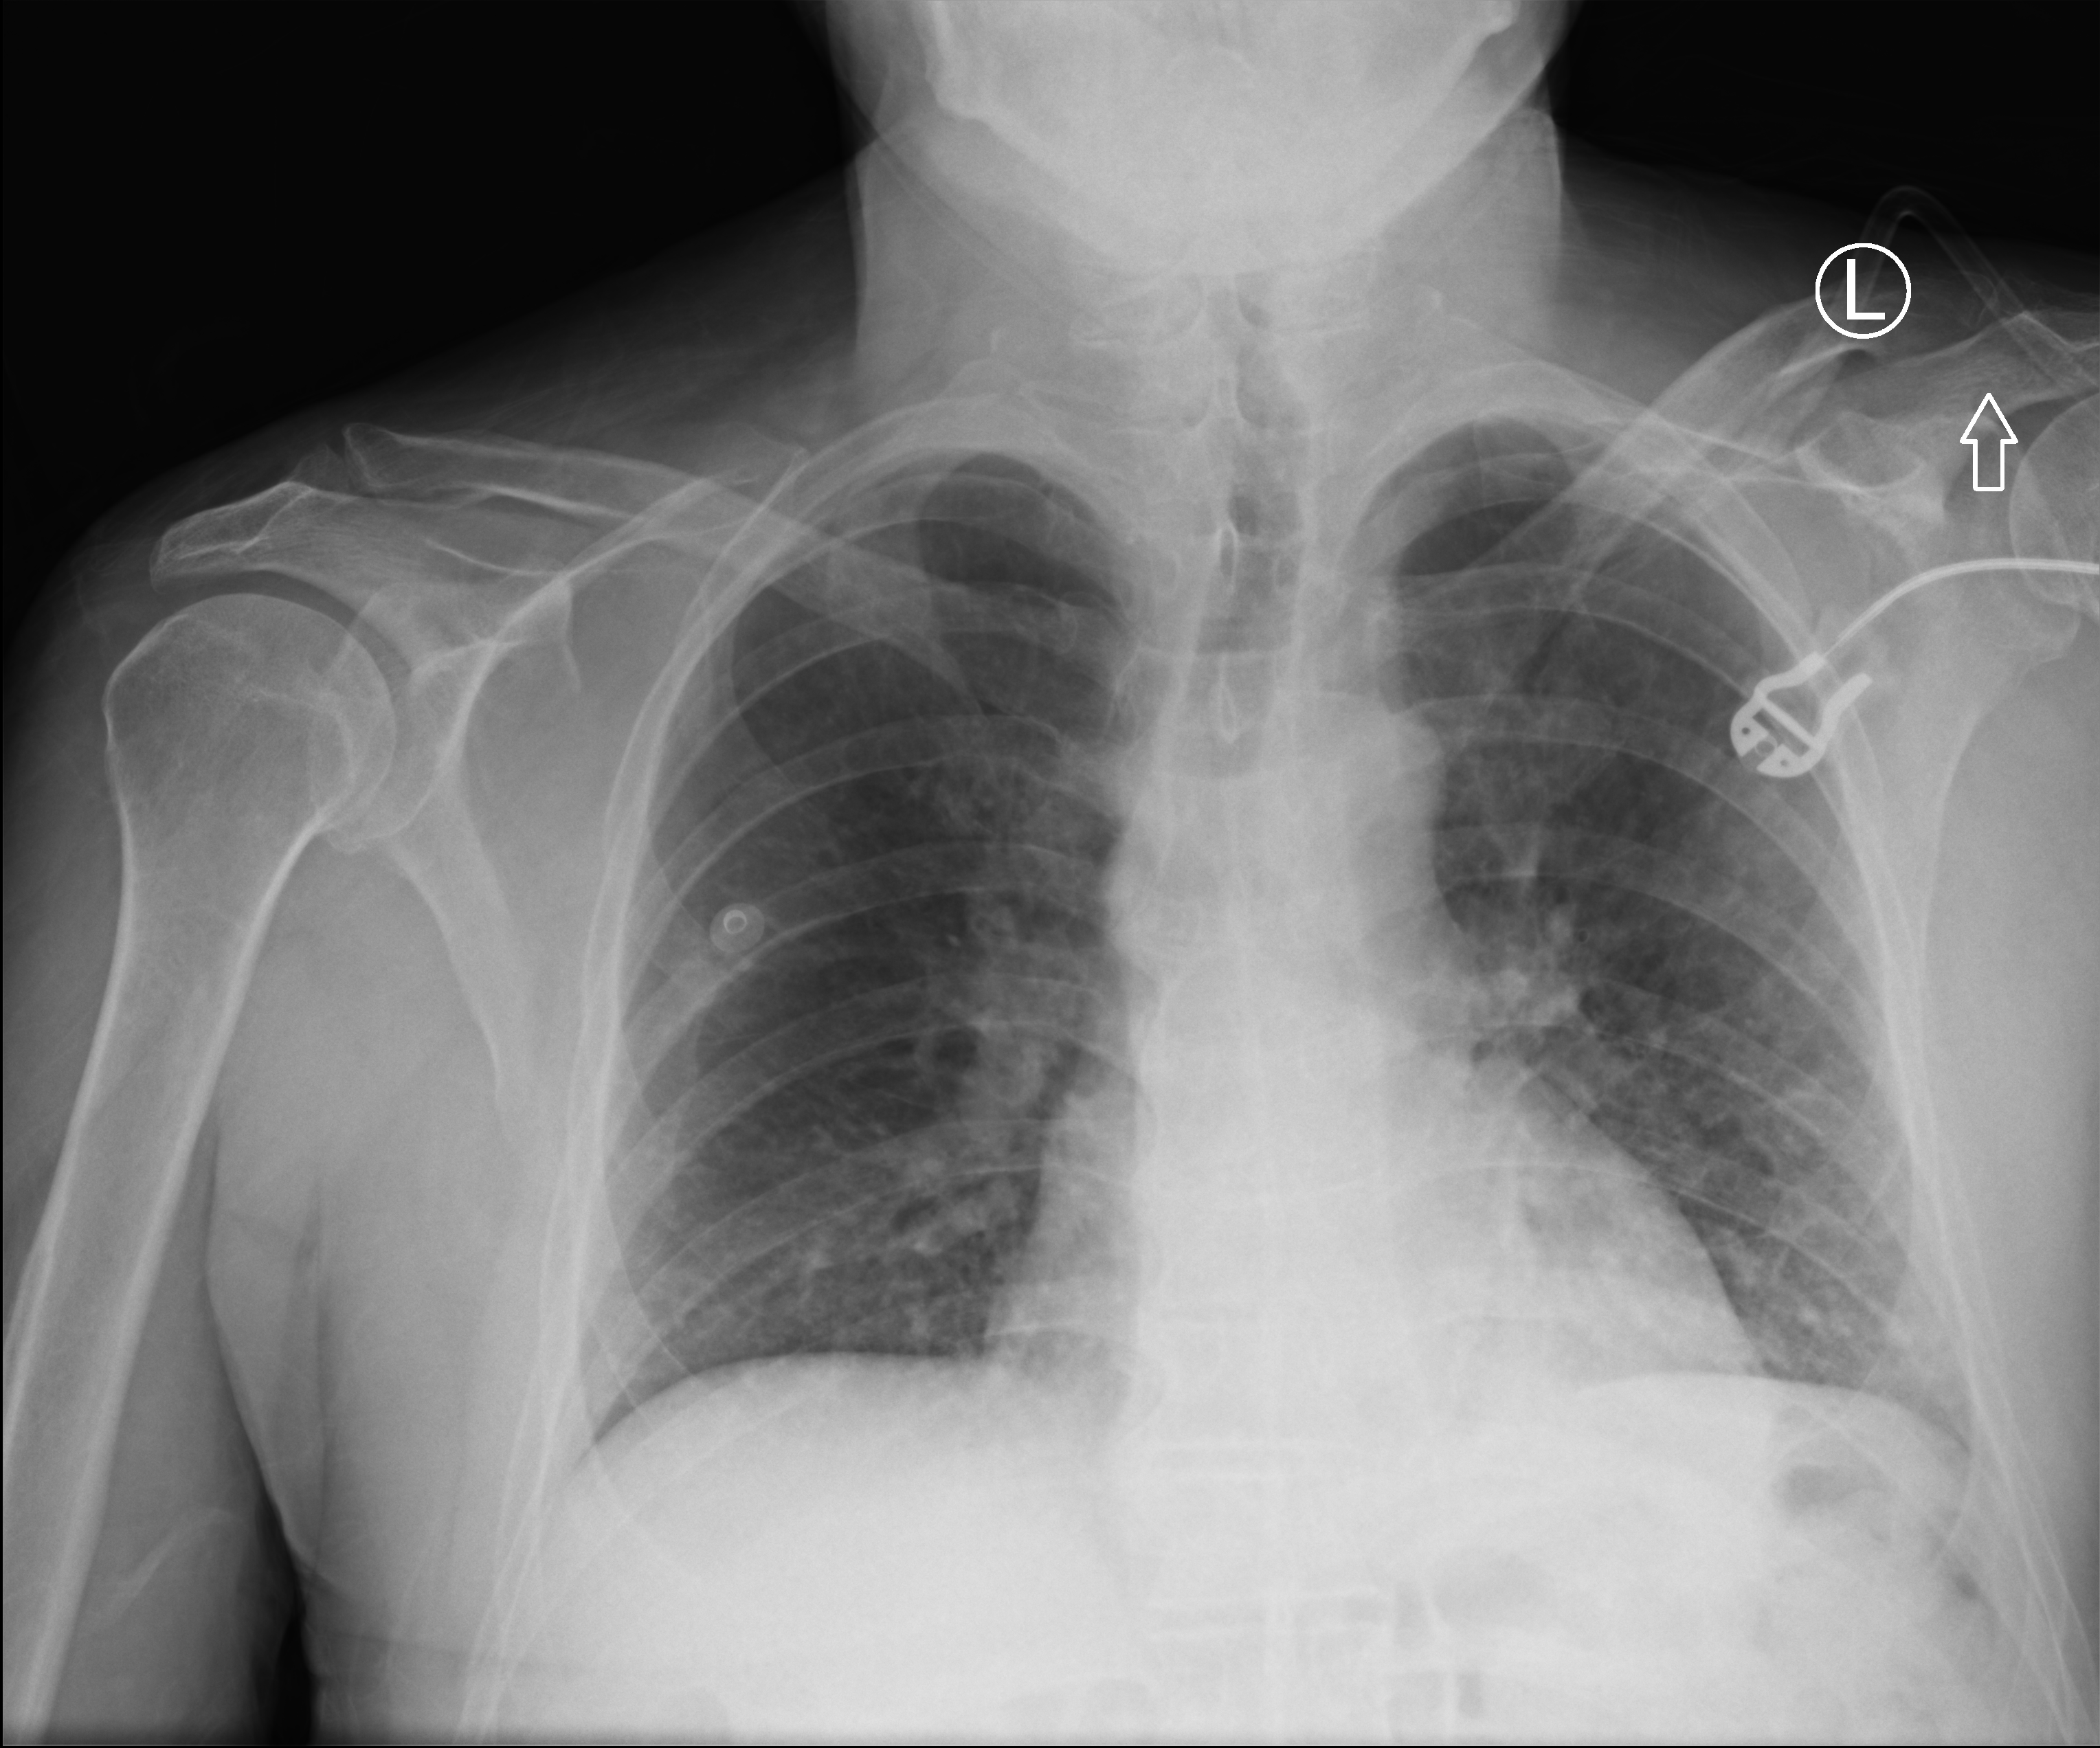
Chest X-ray (portable), anteroposterior (AP) projection. Male patient hospitalised with COVID-19, age 18–59 years.
From the hospital-stay record, not from the radiograph (when in the stay this image was taken is not recorded): mechanically ventilated during this hospital stay: no; admitted to intensive care during this hospital stay: no.